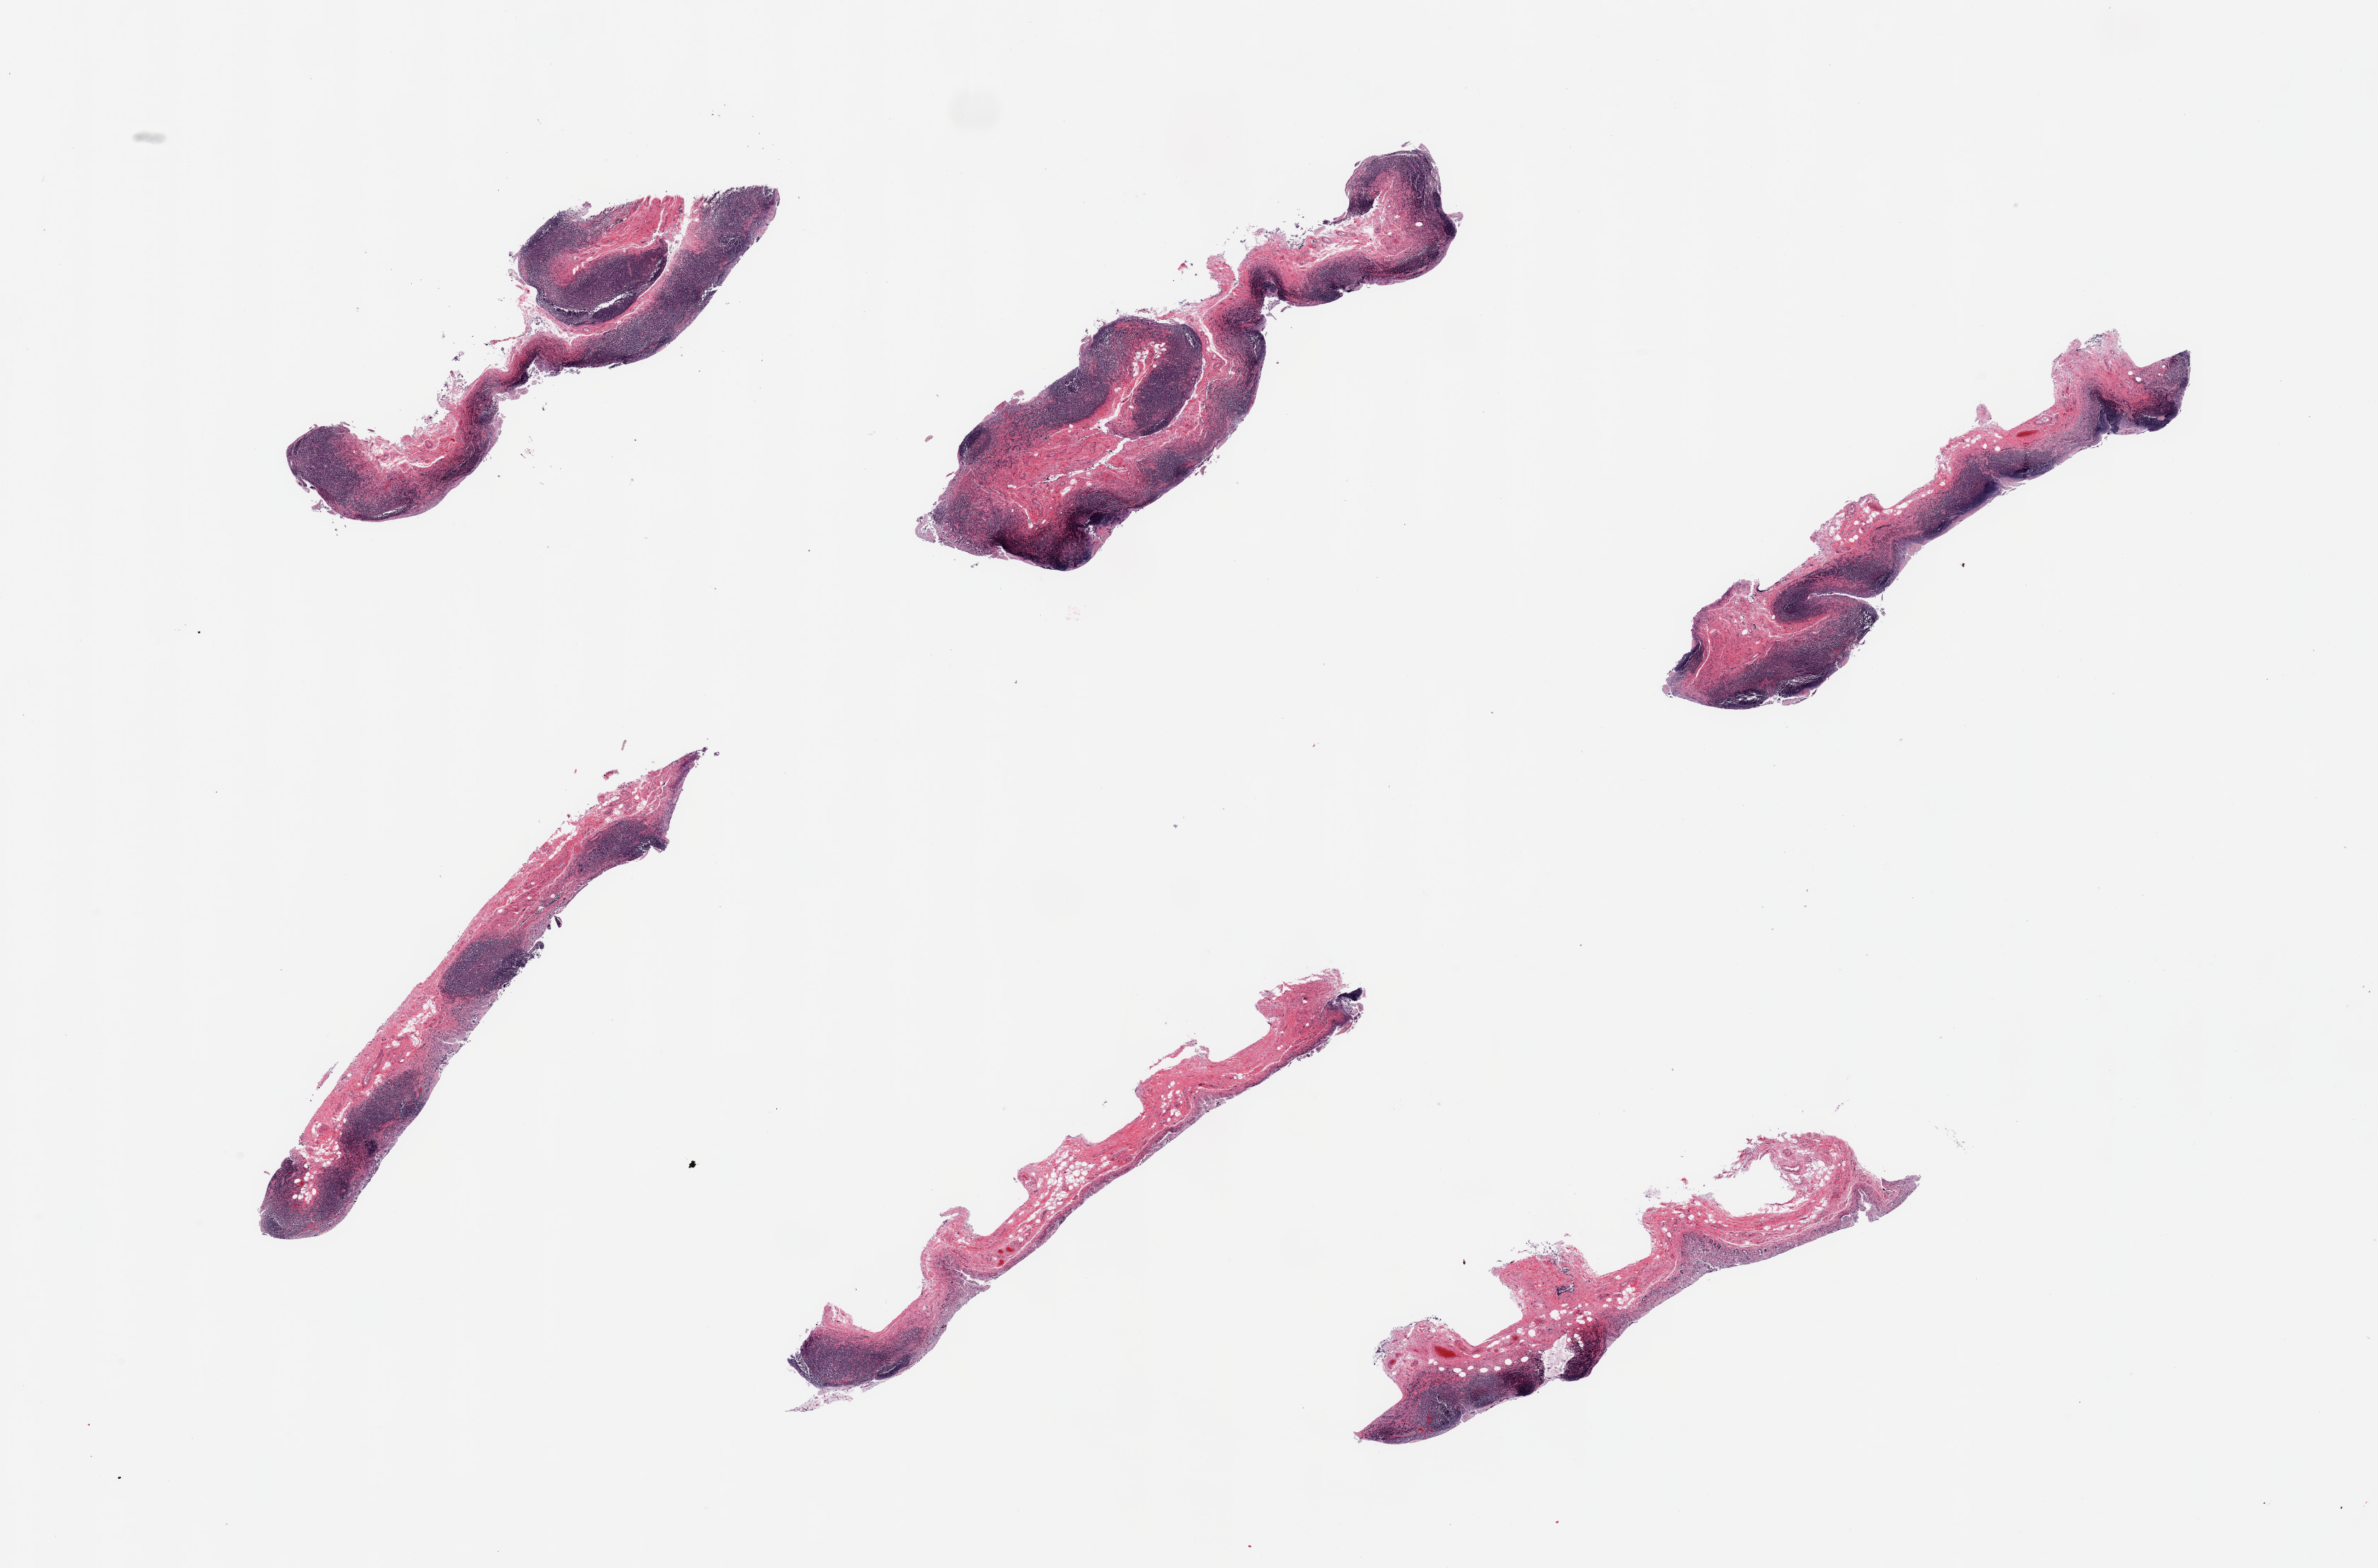
Whole-slide image, haematoxylin and eosin stain, brightfield, low-resolution overview of the scanned area, about 26.6 x 17.5 mm (slide scanned at 20x), PAXgene-fixed paraffin-embedded (PFPE) section, section of ileum (target tissue), donor tissue sample. Male donor.
Review note (as recorded): 6 pieces, advanced glandular autolysis with prominent residual target lymphoid aggregatess, ~40% of tissue.